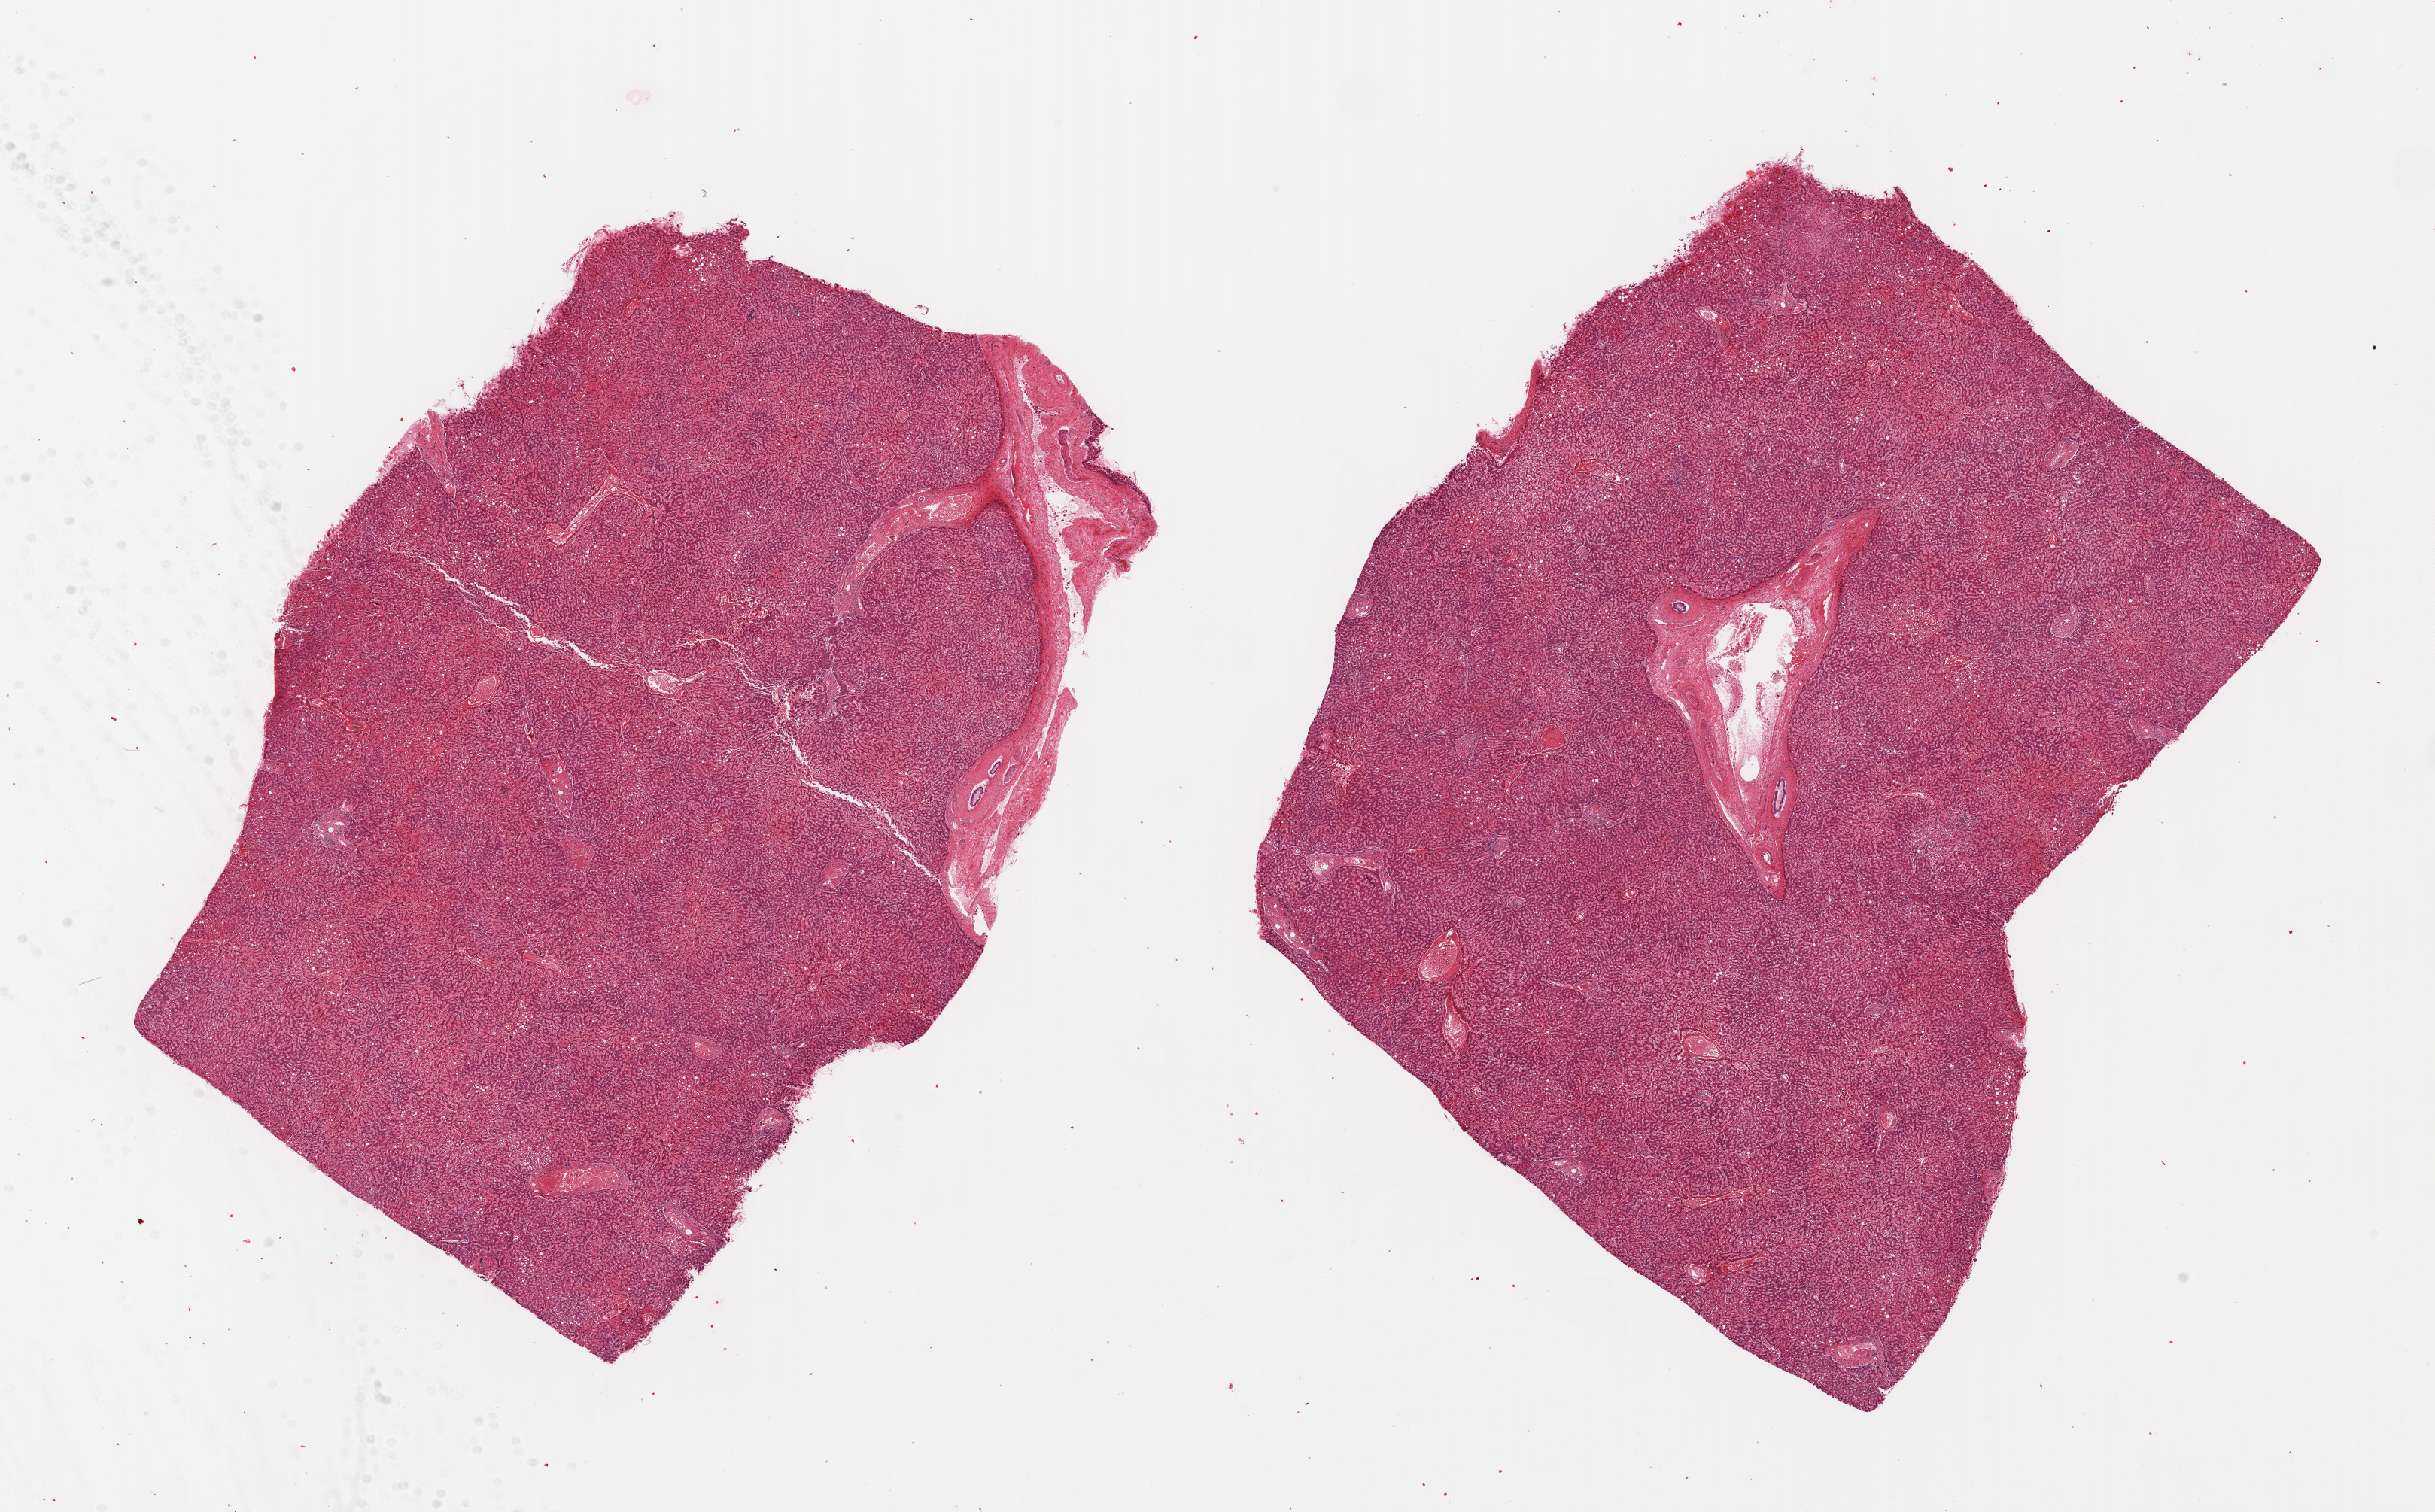
Digitized hematoxylin and eosin (H&E)-stained section, a low-resolution overview of the entire scanned area, about 25.6 x 15.9 mm (slide scanned at 20x). PAXgene-fixed, paraffin-embedded tissue. Target tissue: liver. Tissue donor sample.
- review note (as recorded): 2 pieces; congestion